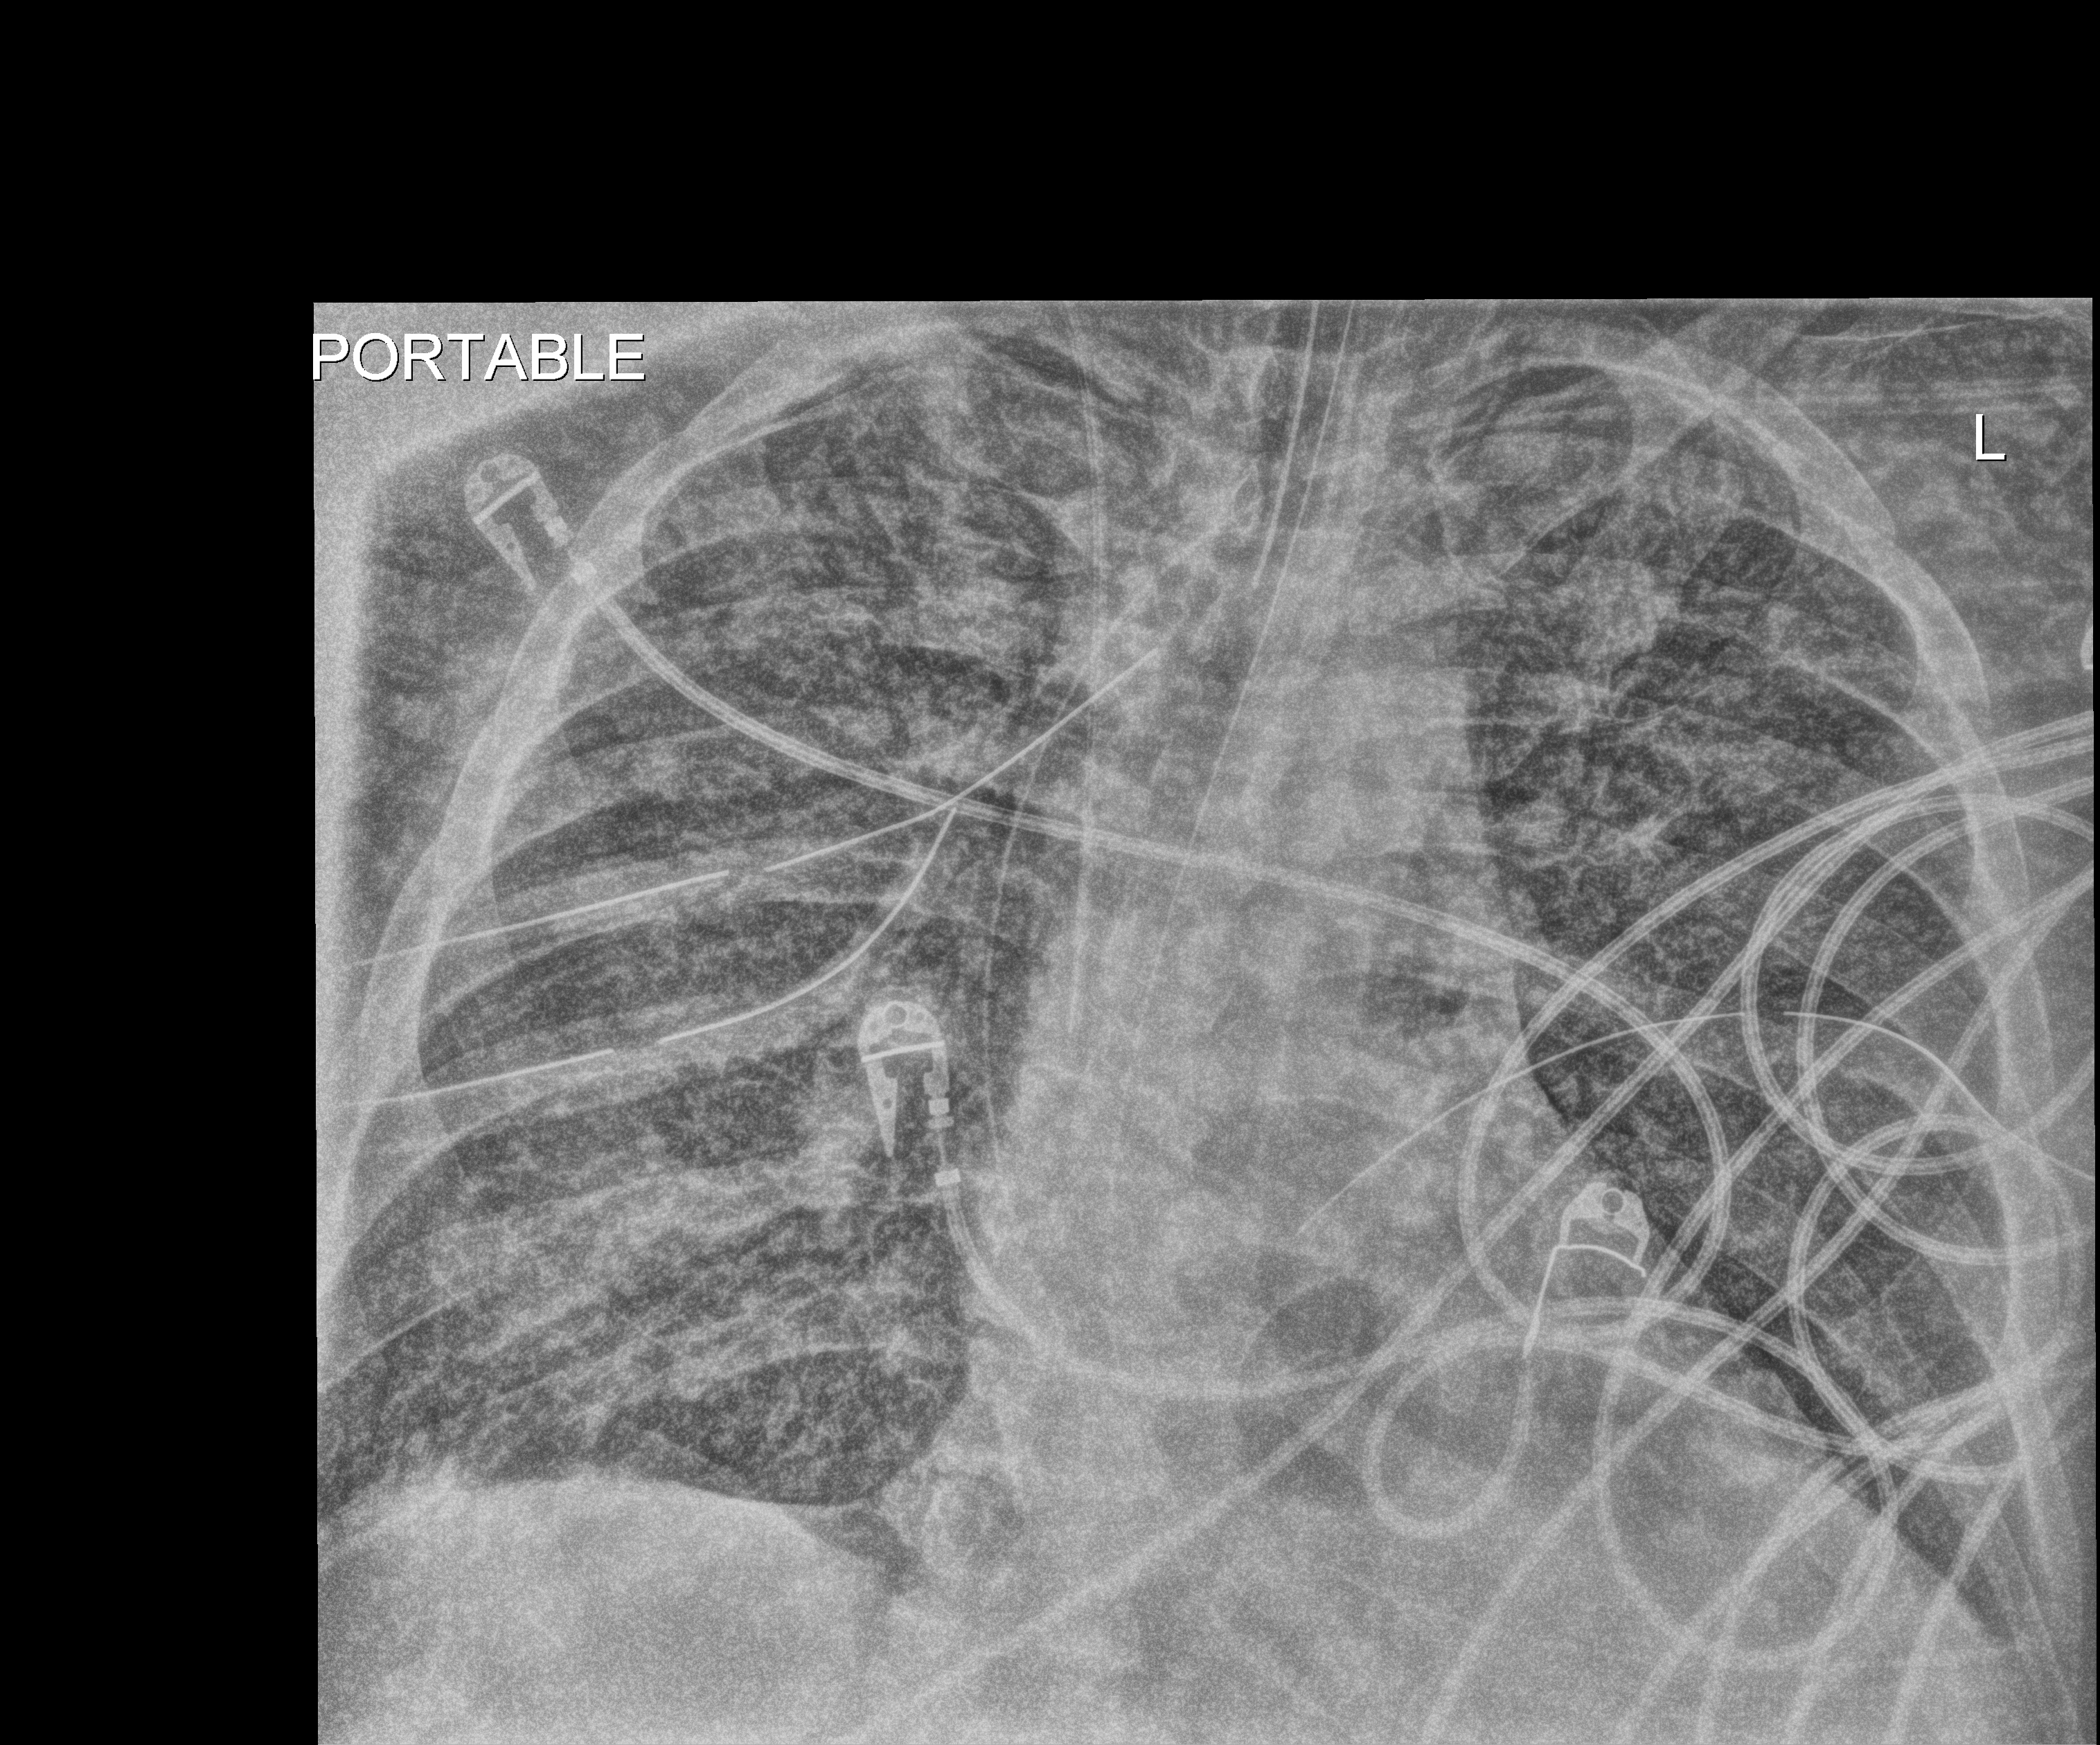
Chest X-ray (portable). Patient hospitalised with COVID-19, aged 18–59 years.
Hospital-stay facts (about this admission, not read from this image; timing relative to this image not recorded): length of hospital stay: 26 days; admitted to intensive care during this hospital stay: yes.